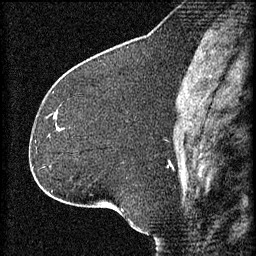
Breast MRI (dynamic contrast-enhanced), one sagittal slice; slice 30 of 60 in the series (ordered by position); 3 images stored at this slice position (order not interpretable as contrast timing); 1.5 T; TE 4.2 ms, TR 8.2 ms; 2 mm slice thickness; 256 × 256 image matrix. Patient: female, 32 years.
Outlined on this slice (semi-automatic segmentation, software-assisted and operator-edited):
- analysis volume of interest (the breast-tissue region the enhancement analysis was run in; not a lesion): box from (x=51, y=114) to (x=66, y=135) px
- tumour enhancement mask (voxels above the 70 % enhancement threshold inside the analysis volume of interest): (x=55, y=116)–(x=57, y=119)